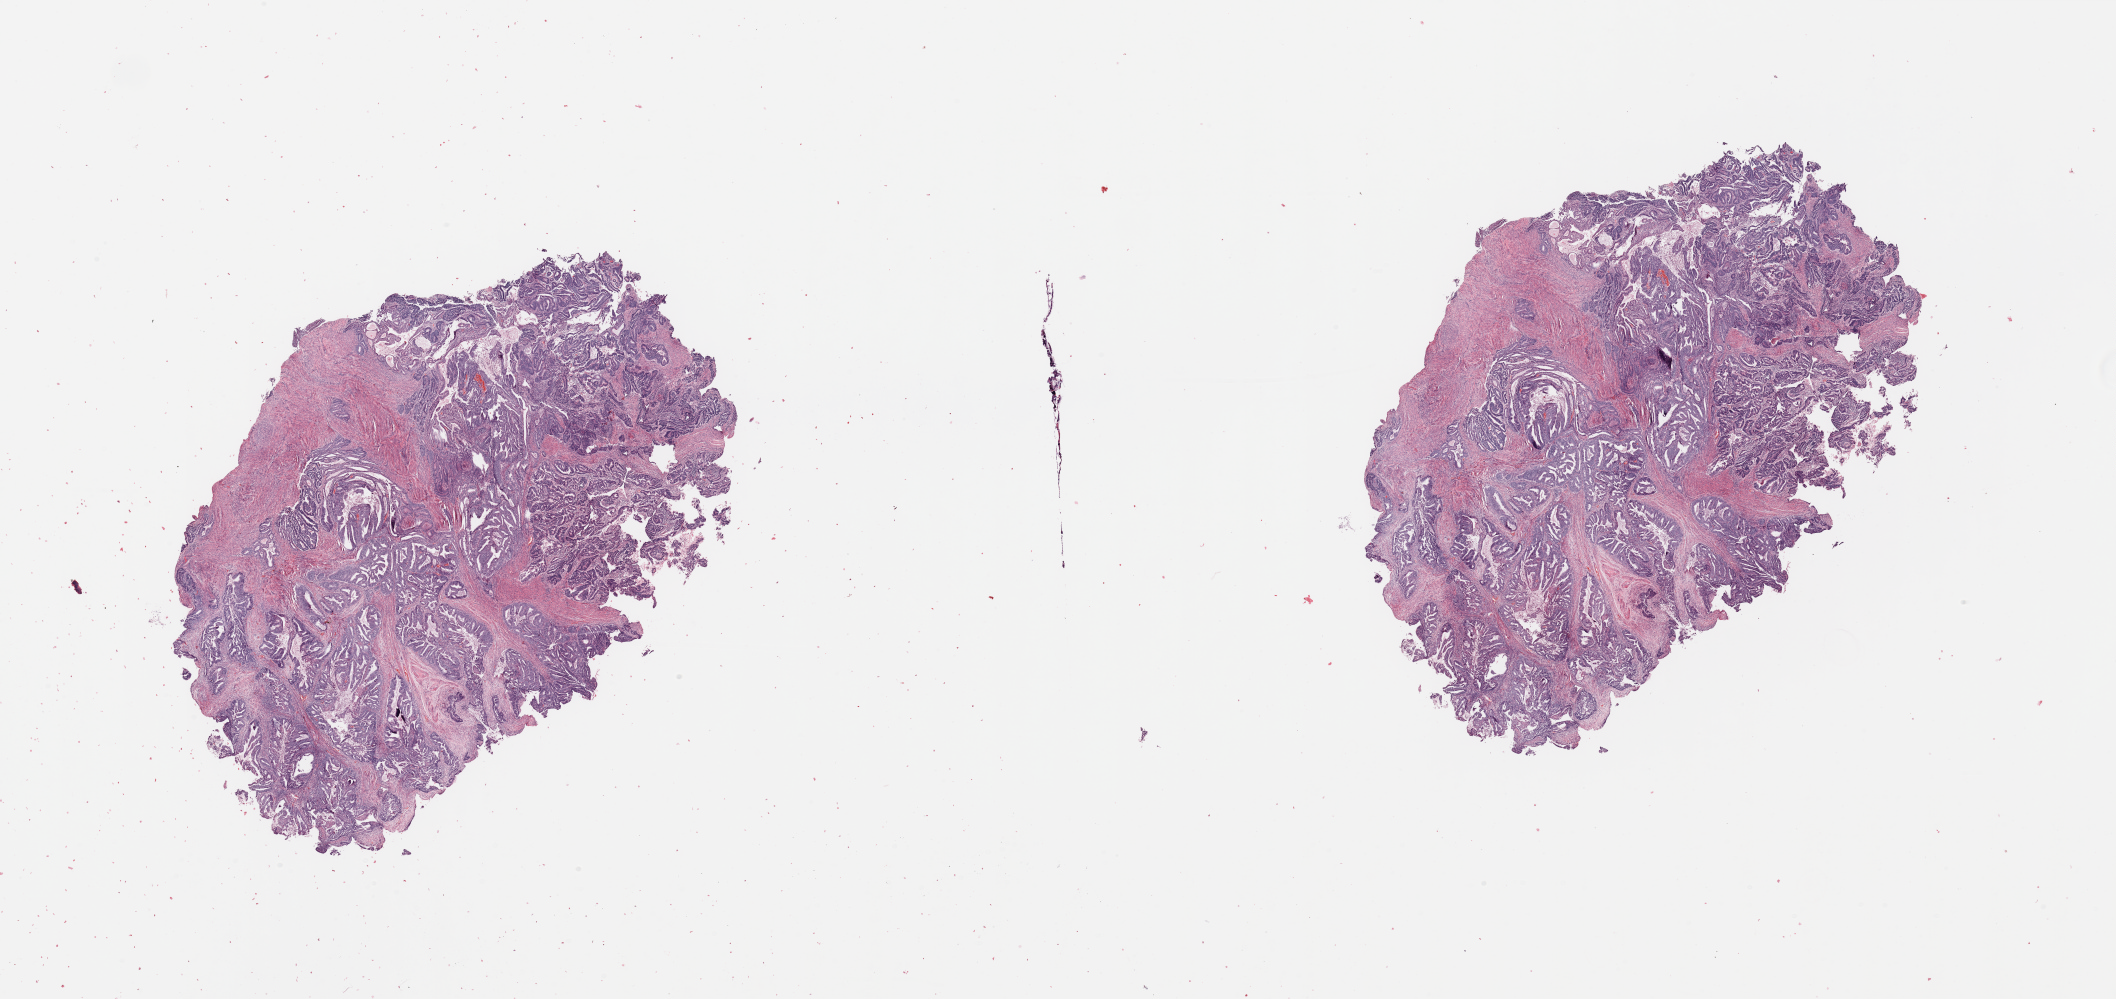
Digitized H&E tissue section (whole slide), low-resolution overview of the scanned area, about 33.5 x 15.8 mm; tumour tissue sample, sampled site: uterus. Female, 53 y/o. Histologic grade: G2 (moderately differentiated). Pathologist review of this section (percent, as recorded): tumour nuclei 80%, necrosis 2%.
AJCC pathologic stage: I. Histologic diagnosis: Endometrioid adenocarcinoma, NOS.